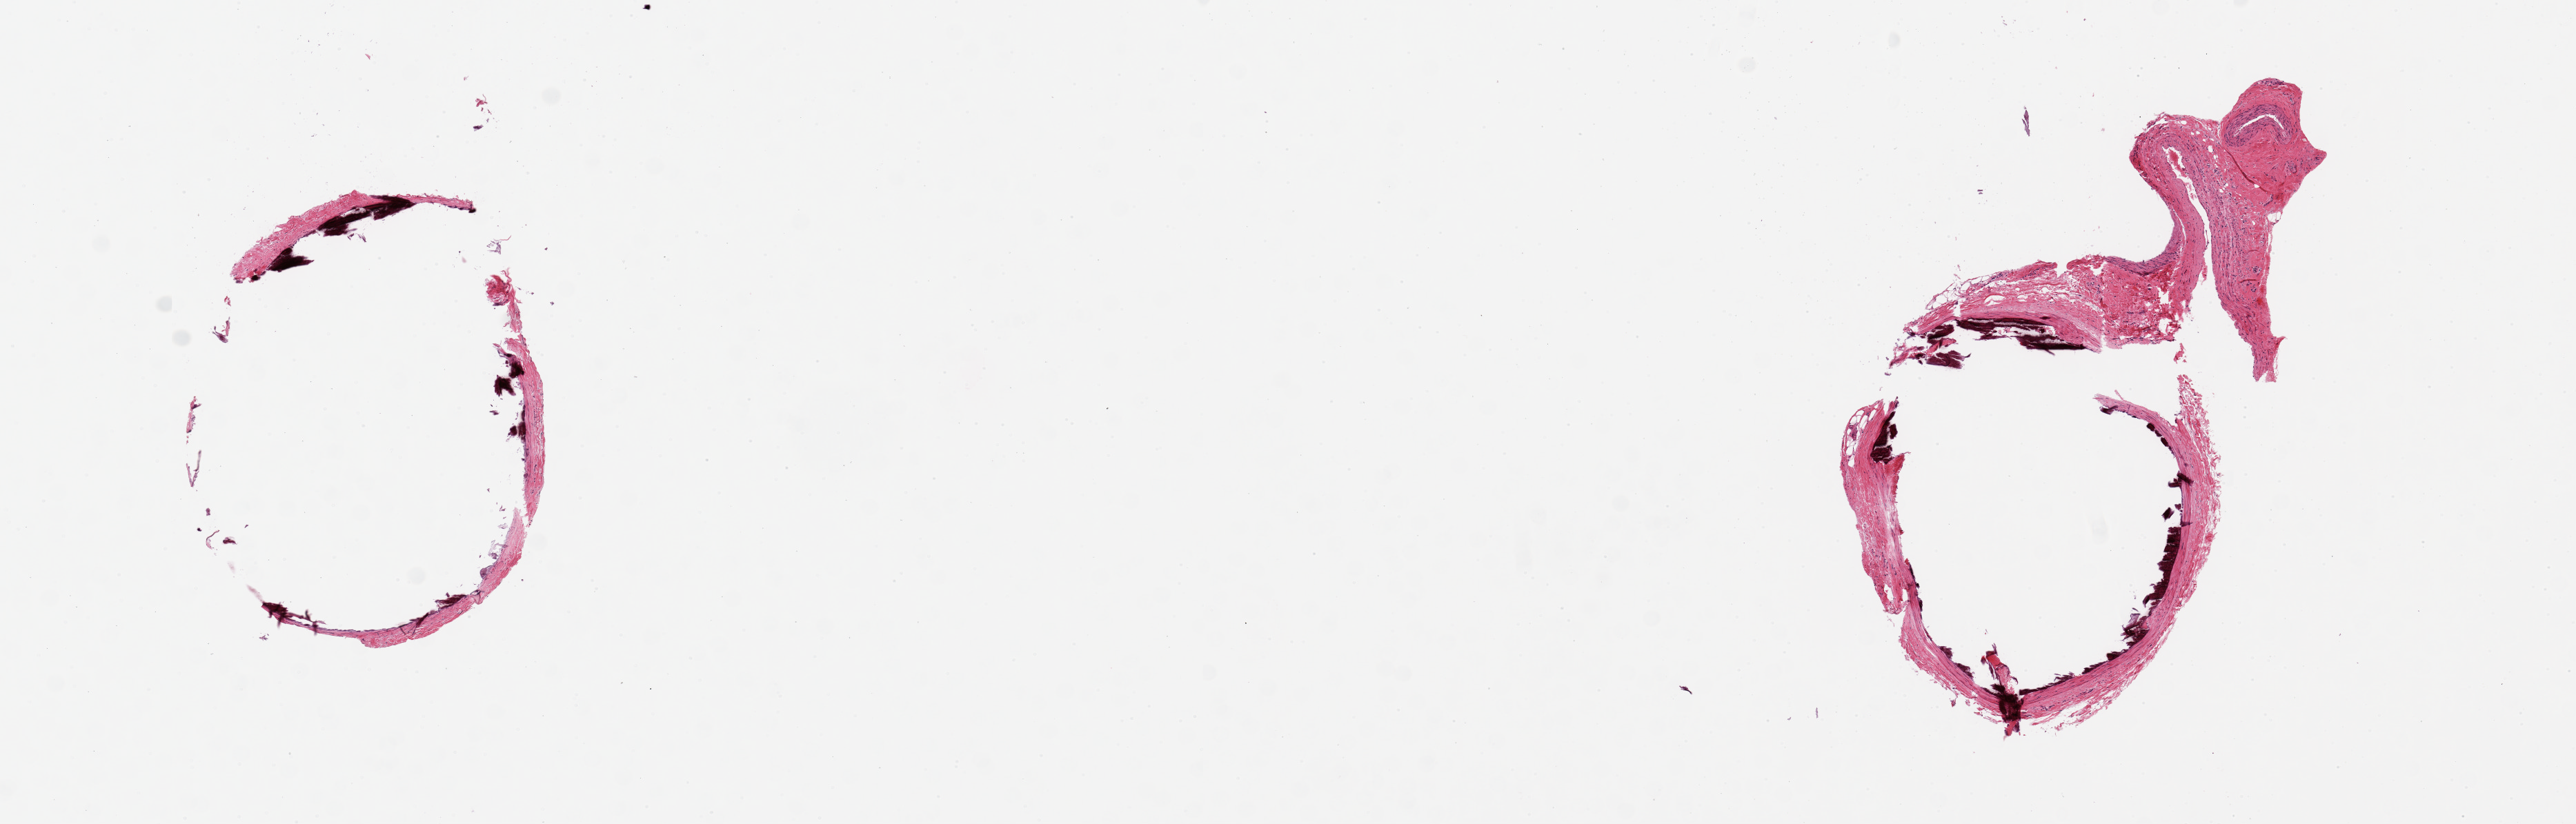
Hematoxylin and eosin (H&E) whole-slide image, brightfield, low-resolution overview of the scanned area, about 14.8 x 4.7 mm. PAXgene-fixed paraffin-embedded (PFPE) section. Sampled site (target tissue): tibial artery. Tissue donor sample.
* pathologist's review note for this sample: 2 pieces ~2.5mm d. Marked circumferential calcification, pattern suggests calcified atherosclerotic deposits rather than Monckeberg's medial sclerosis